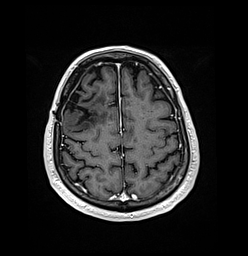
Brain MRI from a brain-tumour surgery series, one axial slice; position 43 of 176 along the scan axis; T1-weighted post-contrast; 1 mm slice thickness; 248 × 256 image matrix, field of view 242 × 250 mm. From the clinical record (not read from this slice): histopathology: Oligodendroglioma; WHO grade: 3; IDH mutation: yes; tumour location: Right Frontal.
Outlined on this slice (outlined manually by an expert reader):
- previous resection cavity: bounding box (x1, y1, x2, y2) in pixels: (65, 90, 90, 124)